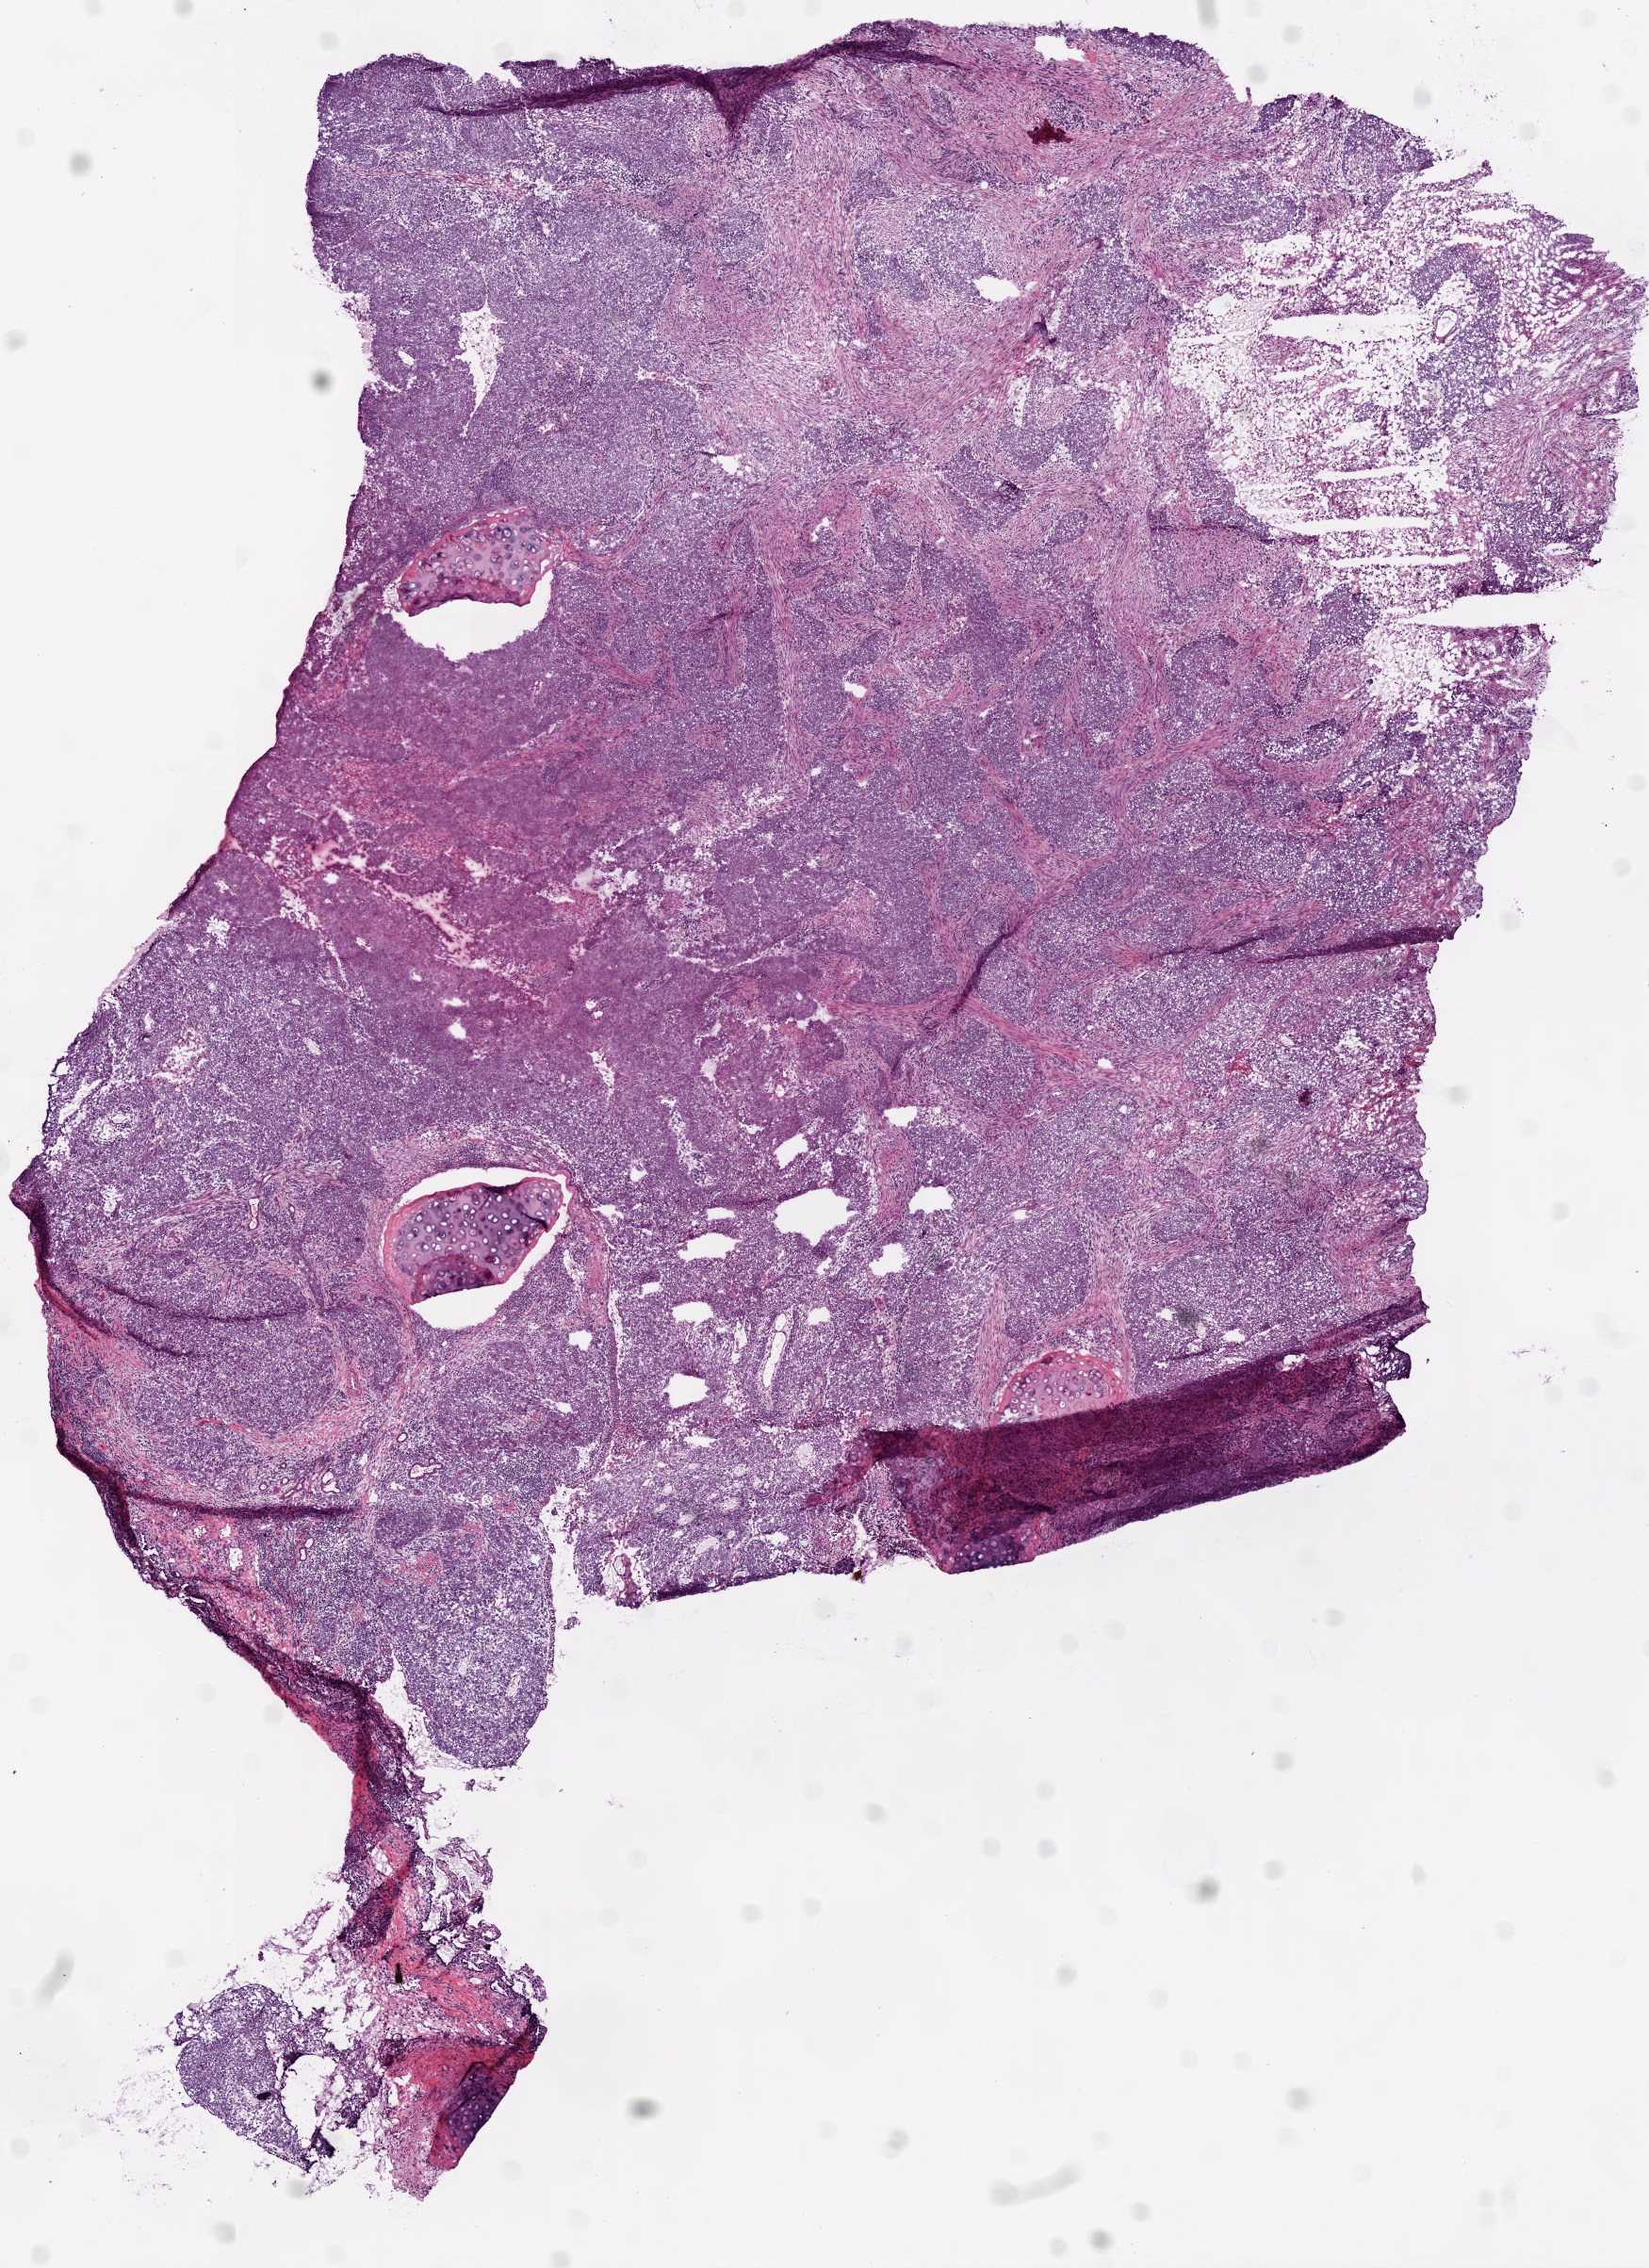
H&E whole-slide image — whole scanned area (about 7.0 x 9.7 mm, from a 20x scan) shown as a low-resolution overview, frozen section, primary tumour sample from the lung. Male patient; age at initial diagnosis 72 years. Pathologist review of this section (percent, as recorded): tumour cells 70%, tumour nuclei 75%, normal cells 5%, stromal cells 15%, necrosis 10%.
- AJCC pathologic stage: IIB
- histologic diagnosis: Squamous cell carcinoma, NOS (upper lobe, lung)